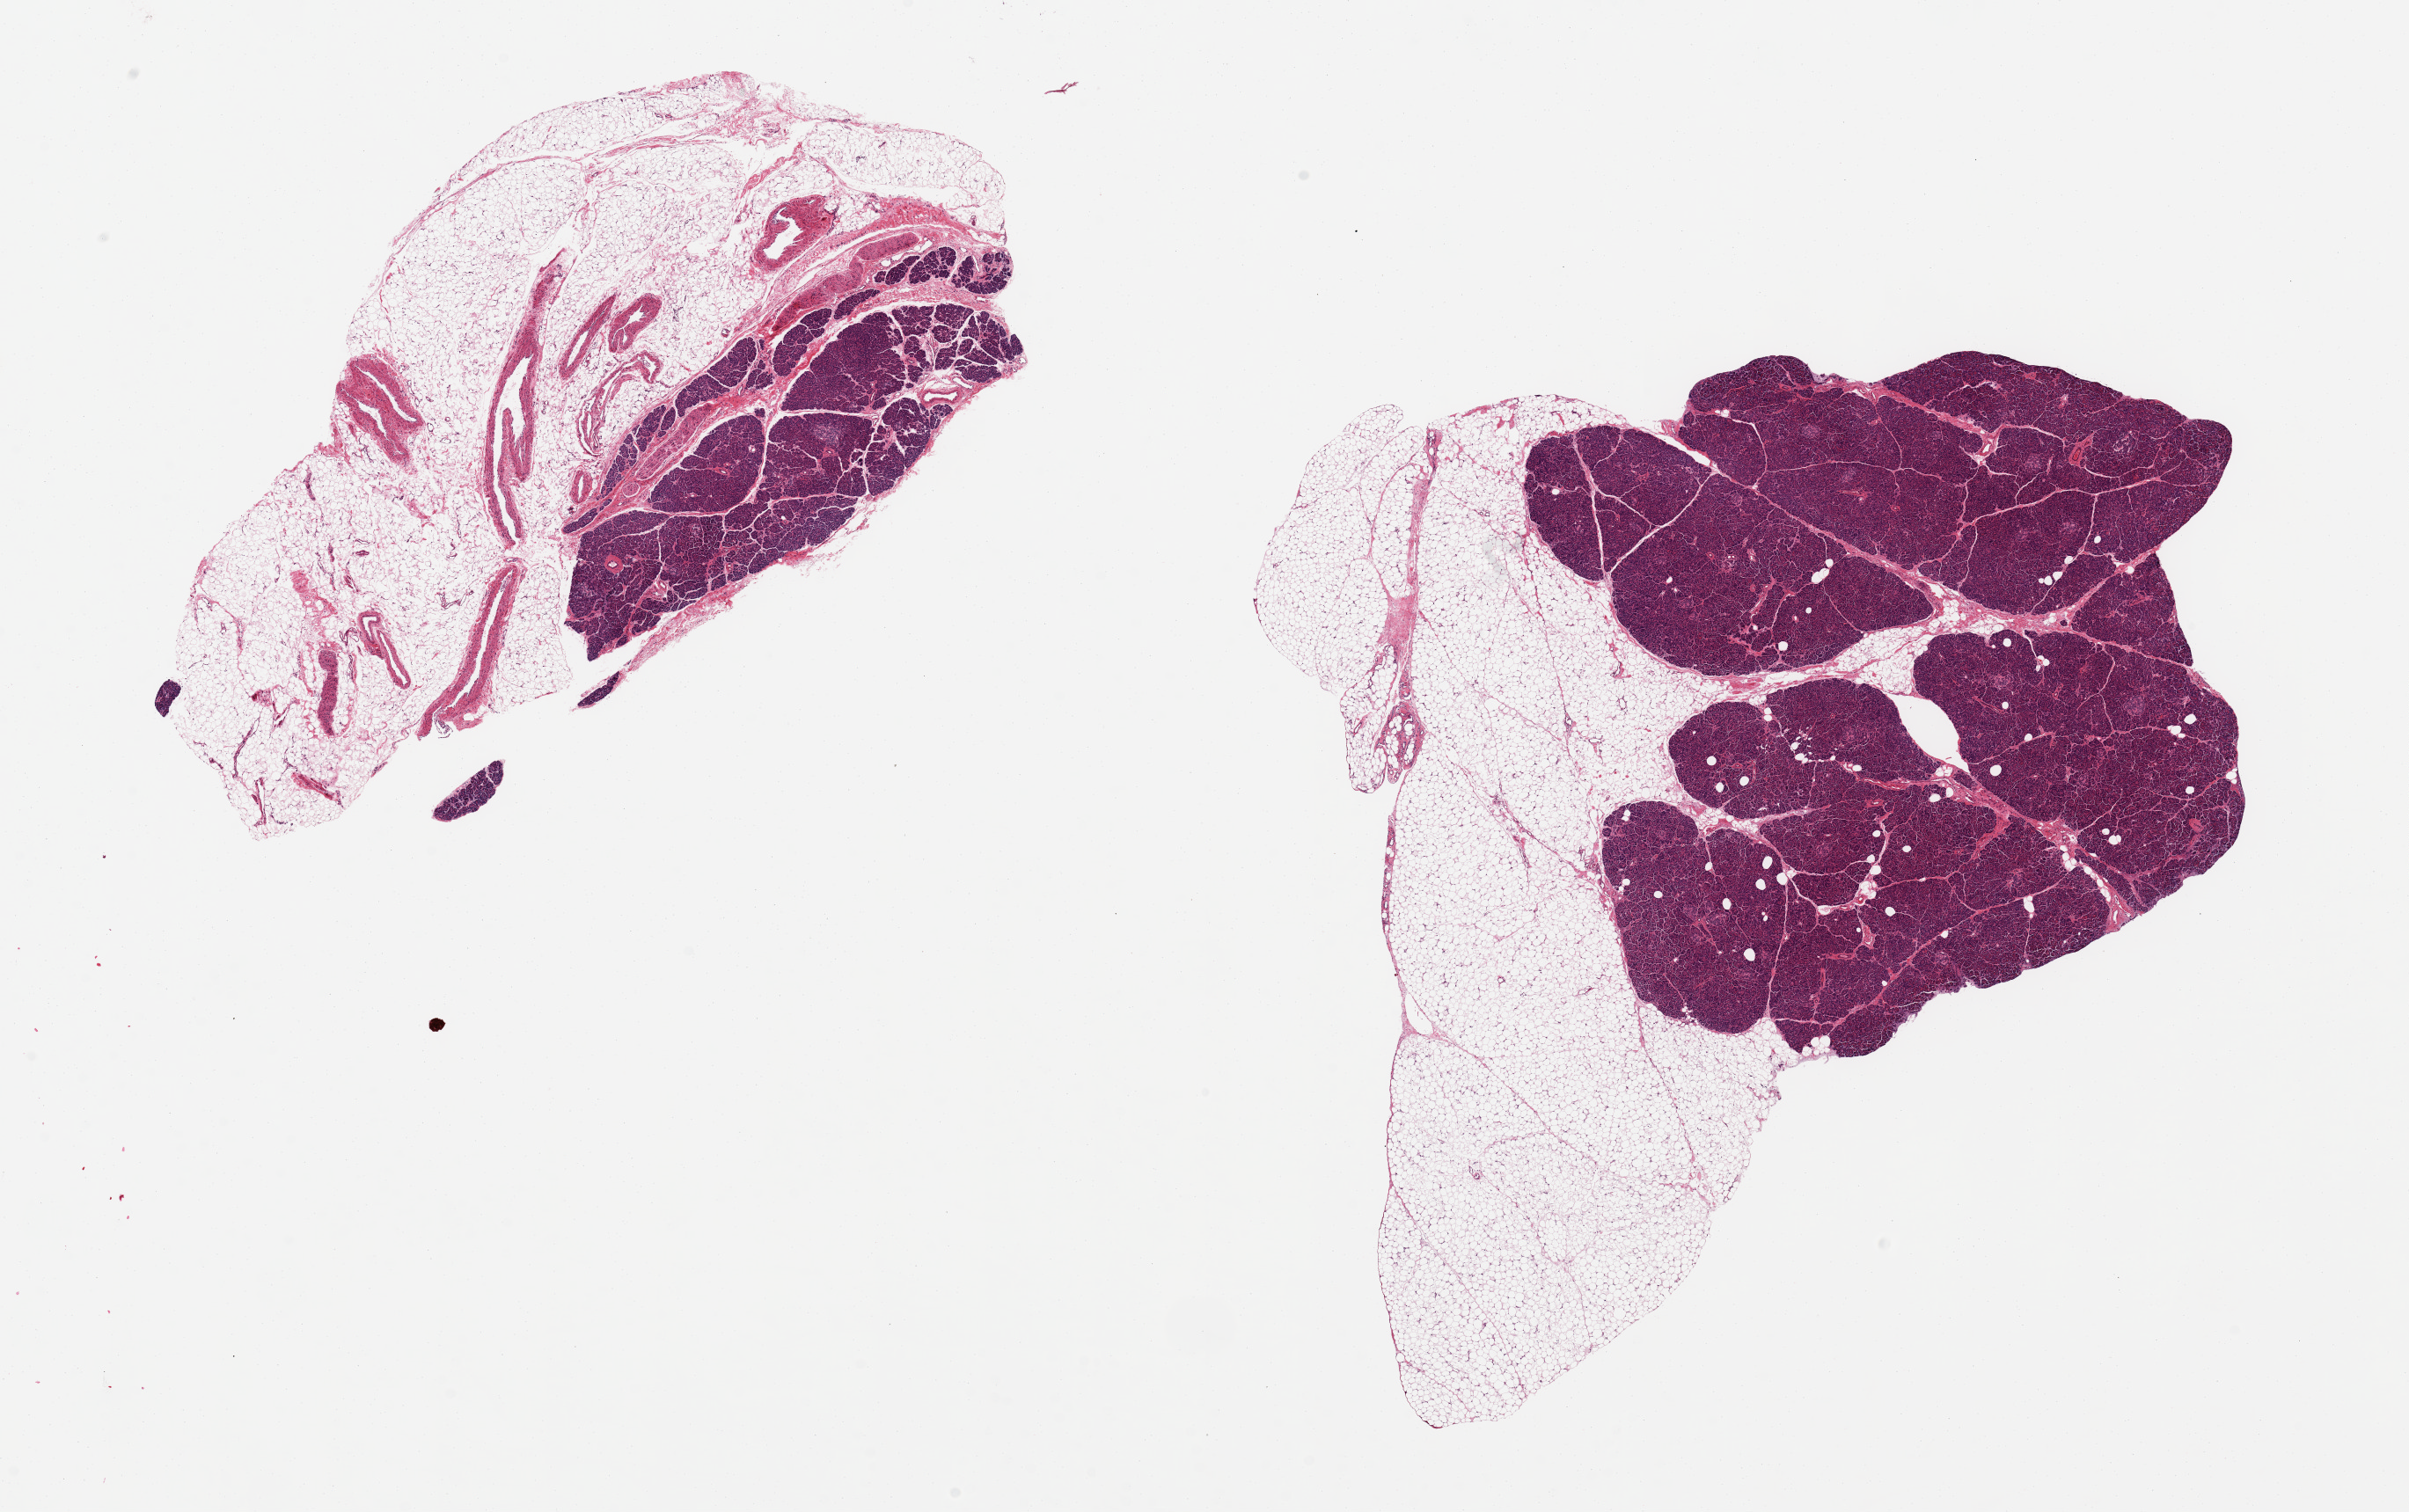
Whole-slide image, haematoxylin and eosin stain, brightfield — a low-resolution overview of the entire scanned area, about 21.7 x 13.6 mm (from a 20x scan). PAXgene-fixed paraffin-embedded (PFPE) section. Target tissue: pancreas. Donor tissue sample. Donor sex: female.
Pathologist's review note for this sample: 2 pieces 9x8 & 8x4 mm; over 50% external adipose tissue.